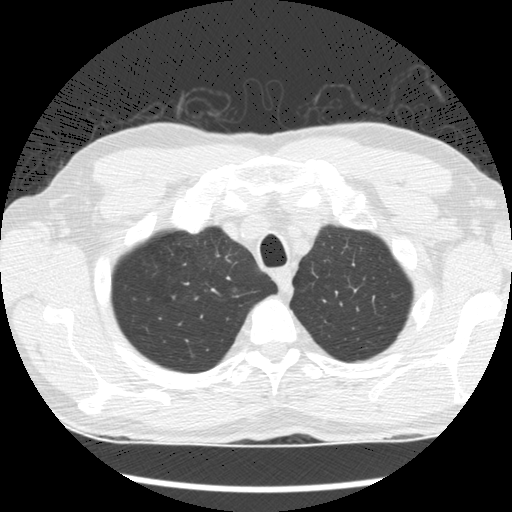
Low-dose screening chest CT, one axial slice; position 137 of 164 along the scan axis; 120 kVp; lung window (W 1500 / L -600 HU); 2.5 mm slice thickness; 512 × 512 image matrix, field of view 340 × 340 mm.
Outlined on this slice (manually delineated by an expert):
- lesion 1 (tumor, upper lobe of right lung): bounding box [x1, y1, x2, y2] px = [233, 286, 239, 293]